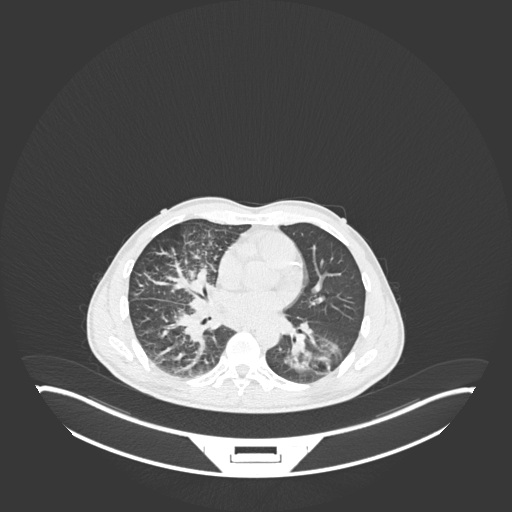
Chest CT, one axial slice. Position 113 of 237 along the scan axis. Lung window (W 1500 / L -600 HU). 512 × 512 image matrix. Patient: male, 49 years. From the clinical record (not read from this slice): clinical TNM (as recorded): T2b N1 M0.
Structures marked on this image (rectangle marked by the reading radiologist):
- lung tumour (recorded histology: adenocarcinoma): bounding box [x1, y1, x2, y2] px = [283, 324, 350, 381]